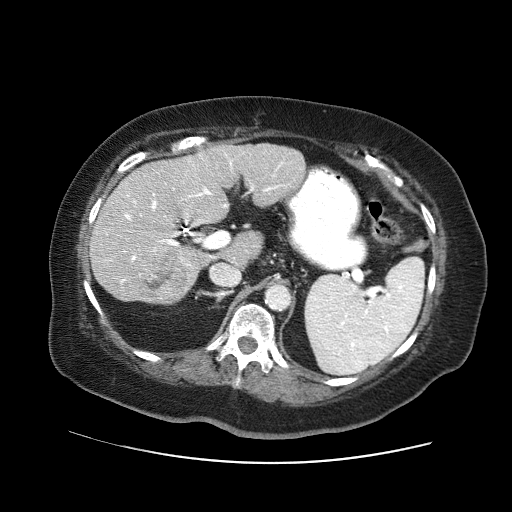
Contrast-enhanced abdominal CT (liver protocol), one axial slice. Slice 28 of 71 in the series (ordered by position). Reconstruction kernel STANDARD. 120 kVp. Soft-tissue window (W 400 / L 40 HU). 2.5 mm slice thickness. 512 × 512 image matrix. From the clinical record (not read from this slice): diagnosis: hepatocellular carcinoma (patient treated with transarterial chemoembolisation; whether this scan precedes or follows treatment is not stated here); TNM stage (as recorded): Stage-II; Child-Pugh class: A; tumour differentiation: poorly differentiated; tumour size: 5 cm.
Outlined on this slice (semi-automatic segmentation, software-assisted and operator-edited):
- liver parenchyma outside the tumour (the mass and vessels are separate outlines, so this box may not span the whole liver): bounding box [x1, y1, x2, y2] px = [90, 144, 304, 304]
- mass: [136, 246, 188, 298]
- liver vessels: [121, 160, 283, 284]